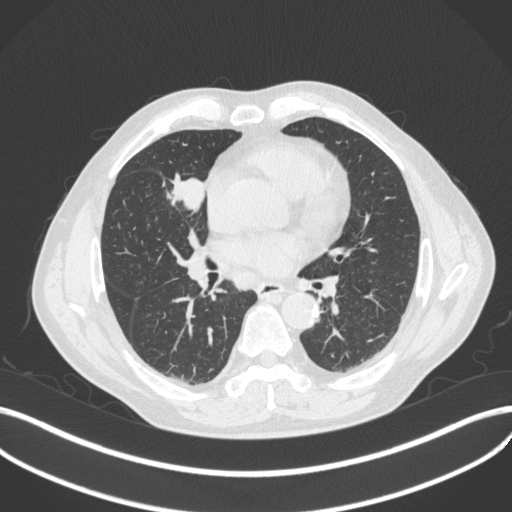
Chest CT, one axial slice. Position 199 of 429 along the scan axis. 120 kVp. Lung window (W 1500 / L -600 HU). 1 mm slice thickness. 512 × 512 image matrix. Male patient, age 61 years. Case-level facts recorded for this patient, not image findings: clinical TNM (as recorded): T2b N1 M0.
Annotated regions visible in this slice (rectangle marked by the reading radiologist):
- lung tumour (recorded histology: squamous cell carcinoma): box from (x=165, y=168) to (x=207, y=215) px